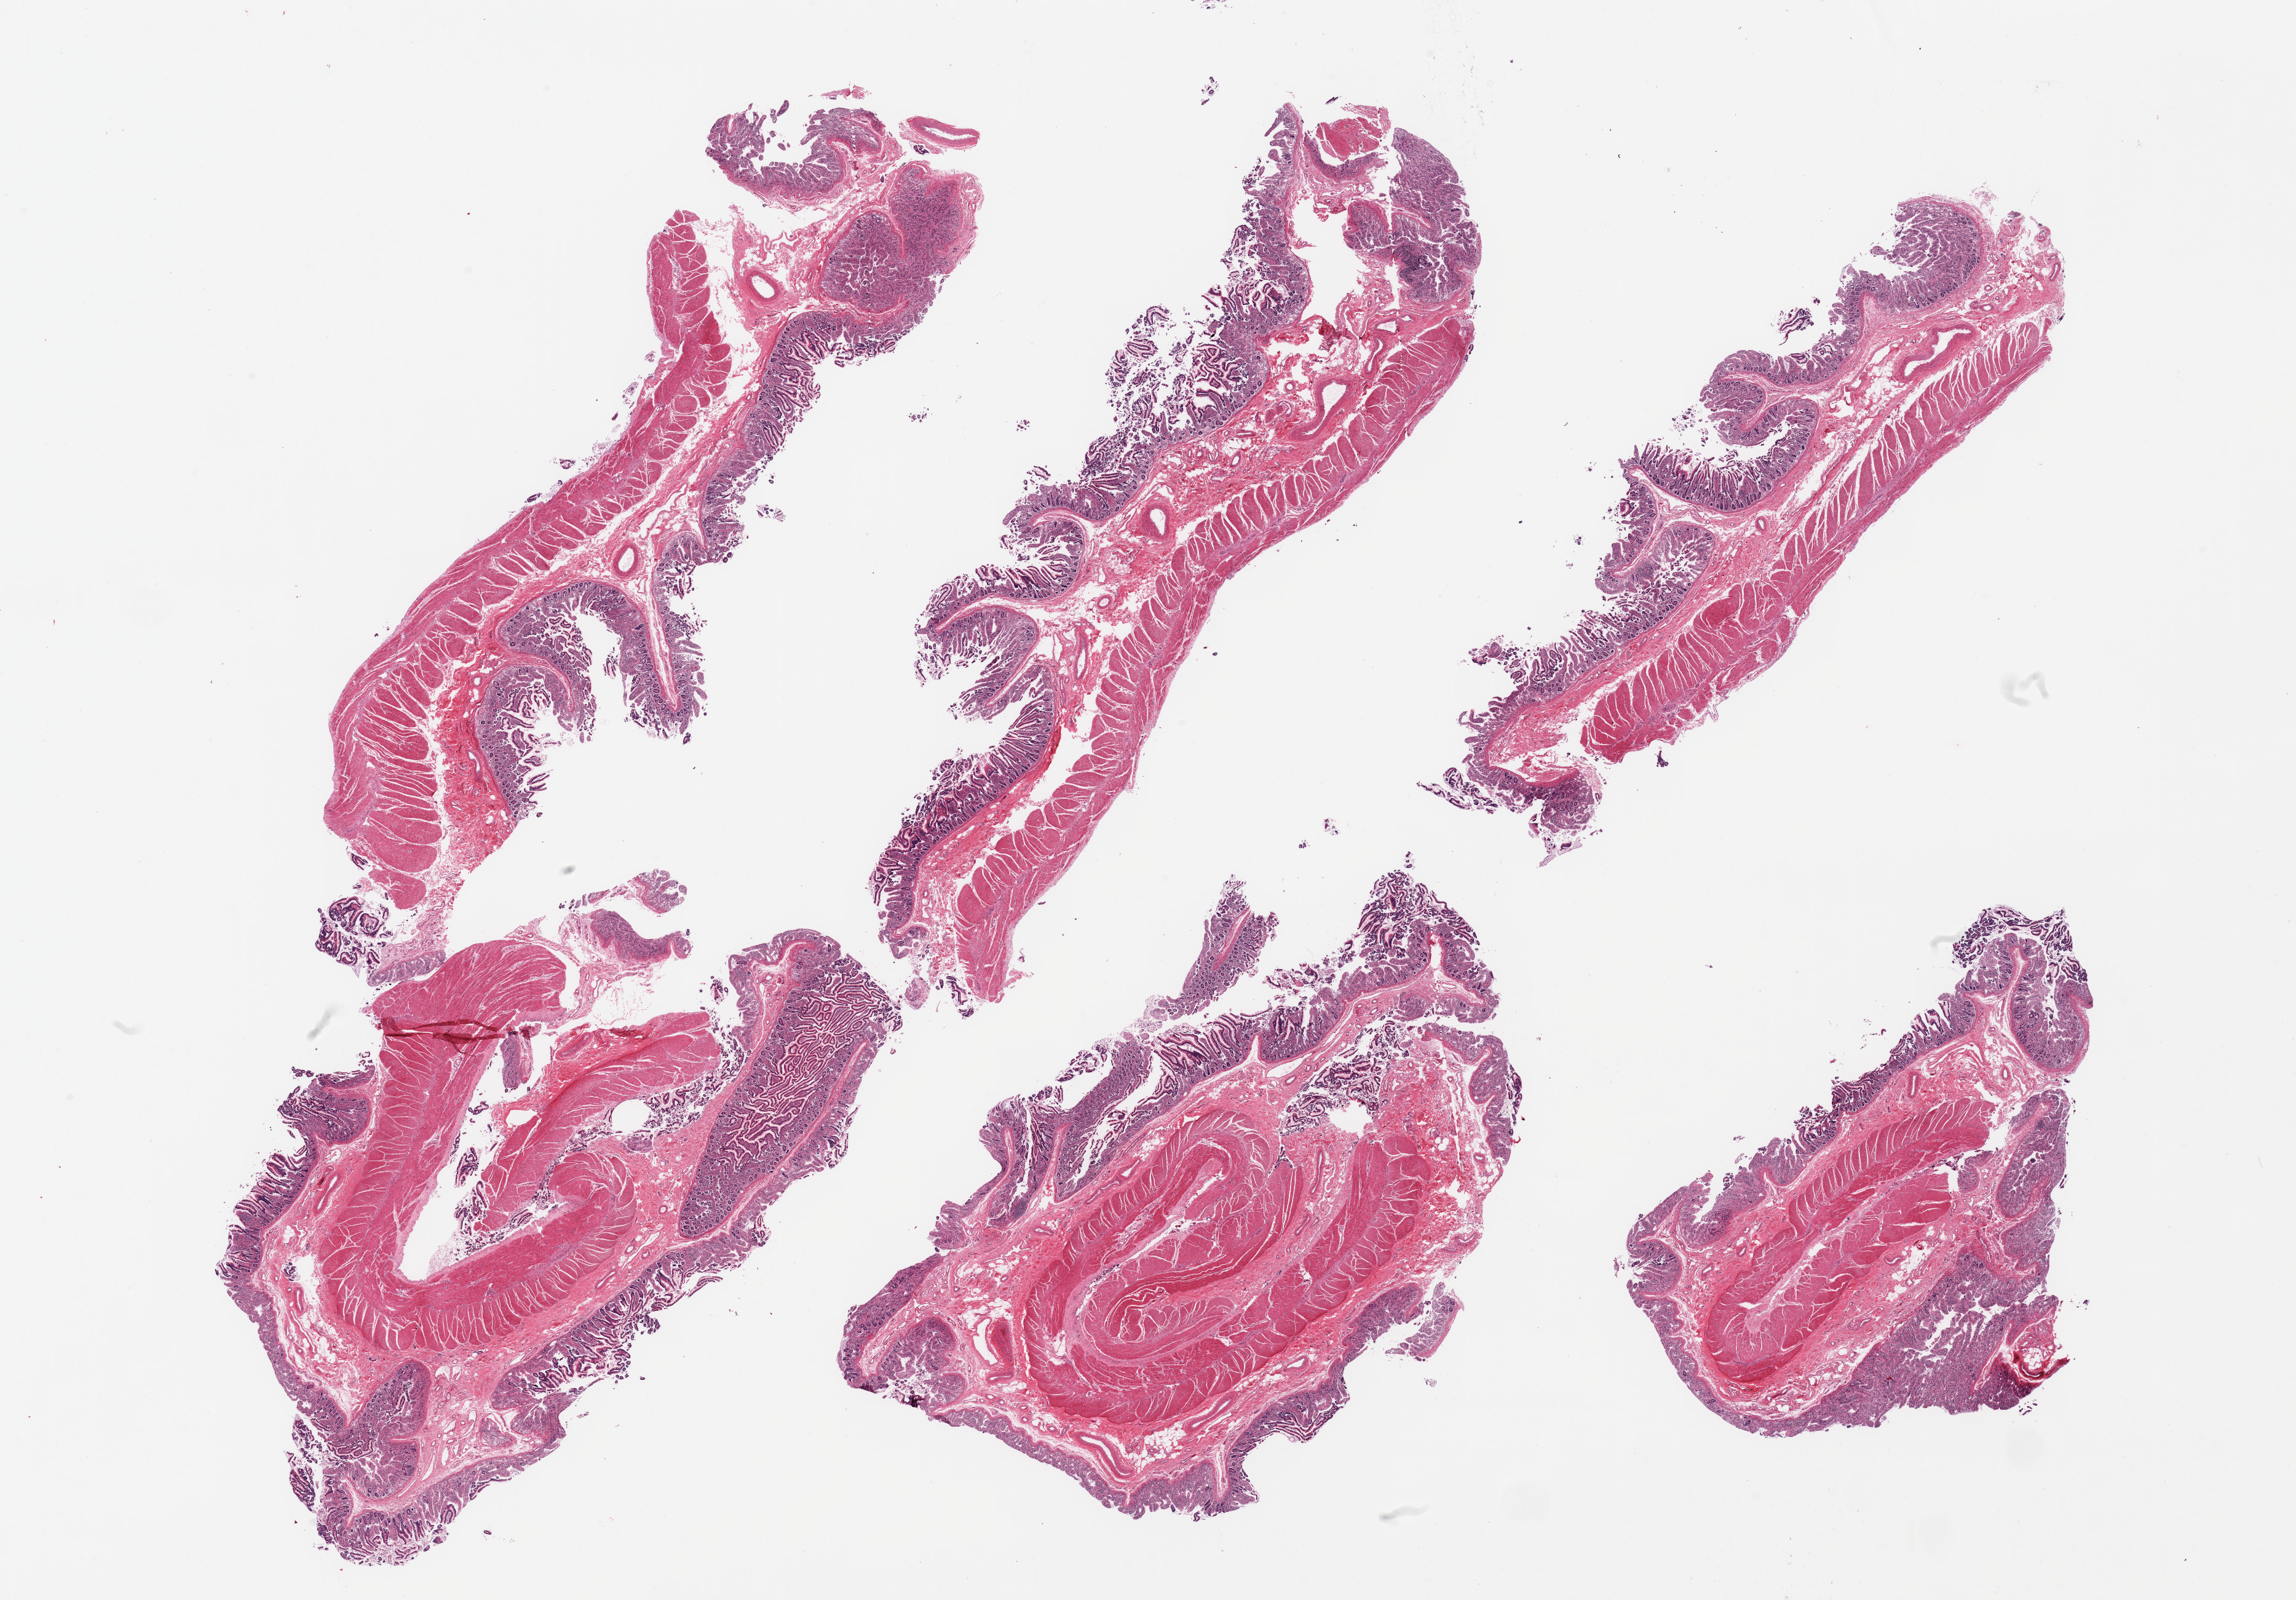
H&E whole-slide image, low-resolution overview of the scanned area, about 29.5 x 20.6 mm. PAXgene-fixed, paraffin-embedded tissue. Section of transverse colon (target tissue). Donor tissue sample.
Review note (as recorded): 6 pieces; full thickness sections of ileum, no lymphoid tissue.